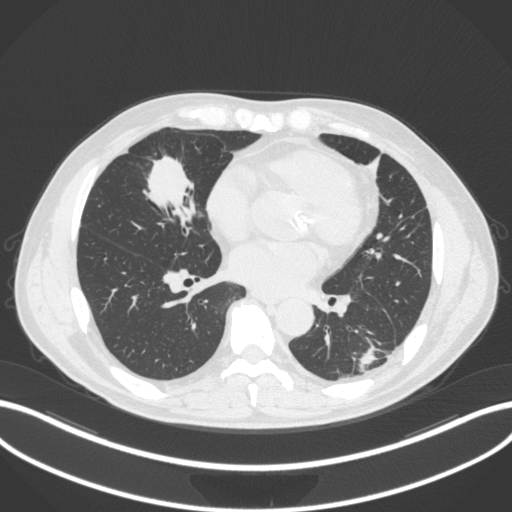
Chest CT, one axial slice; position 125 of 399 along the scan axis; 120 kVp; lung window (W 1500 / L -600 HU); 1 mm slice thickness; 512 × 512 image matrix, field of view 400 × 400 mm. Male patient, age 59 years. Case-level facts recorded for this patient, not image findings: clinical TNM (as recorded): T2a N1 M0.
Structures marked on this image (bounding box drawn by a radiologist):
- lung tumour (recorded histology: adenocarcinoma): box from (x=134, y=147) to (x=200, y=225) px